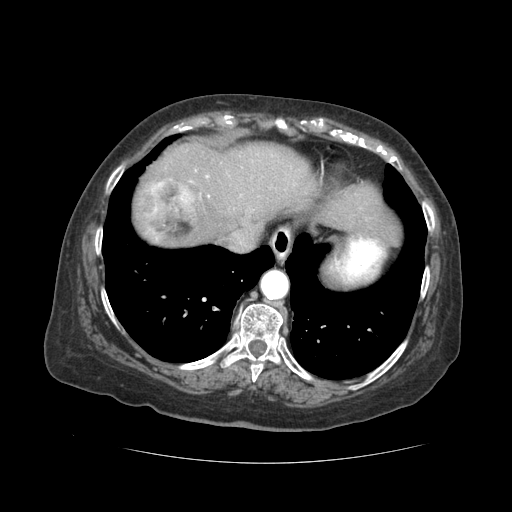
Contrast-enhanced abdominal CT (liver protocol), one axial slice; position 42 of 59 along the scan axis; soft-tissue window (W 400 / L 40 HU); 512 × 512 image matrix, field of view 380 × 380 mm. Case-level facts recorded for this patient, not image findings: diagnosis: hepatocellular carcinoma (patient treated with transarterial chemoembolisation; whether this scan precedes or follows treatment is not stated here); TNM stage (as recorded): Stage-I; Child-Pugh class: A.
Annotated regions visible in this slice (semi-automatic segmentation, software-assisted and operator-edited):
- liver parenchyma outside the tumour (the mass and vessels are separate outlines, so this box may not span the whole liver): box from (x=132, y=142) to (x=396, y=246) px
- mass: (x=143, y=179)–(x=197, y=241)
- liver vessels: (x=206, y=175)–(x=209, y=197)